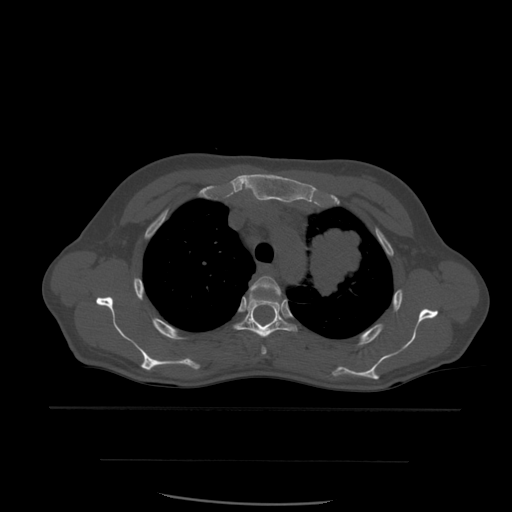
CT including the spine, one axial slice; slice 430 of 574 in the series (ordered by position); bone window (W 1800 / L 400 HU); 1.25 mm slice thickness; 512 × 512 image matrix. Patient age 48 years. Case-level facts recorded for this patient, not image findings: primary cancer: lung.
Annotated regions visible in this slice (semi-automatic segmentation, software-assisted and operator-edited):
- T3 vertebra: box from (x=250, y=276) to (x=282, y=355) px
- T4 vertebra: (x=234, y=297)–(x=298, y=338)